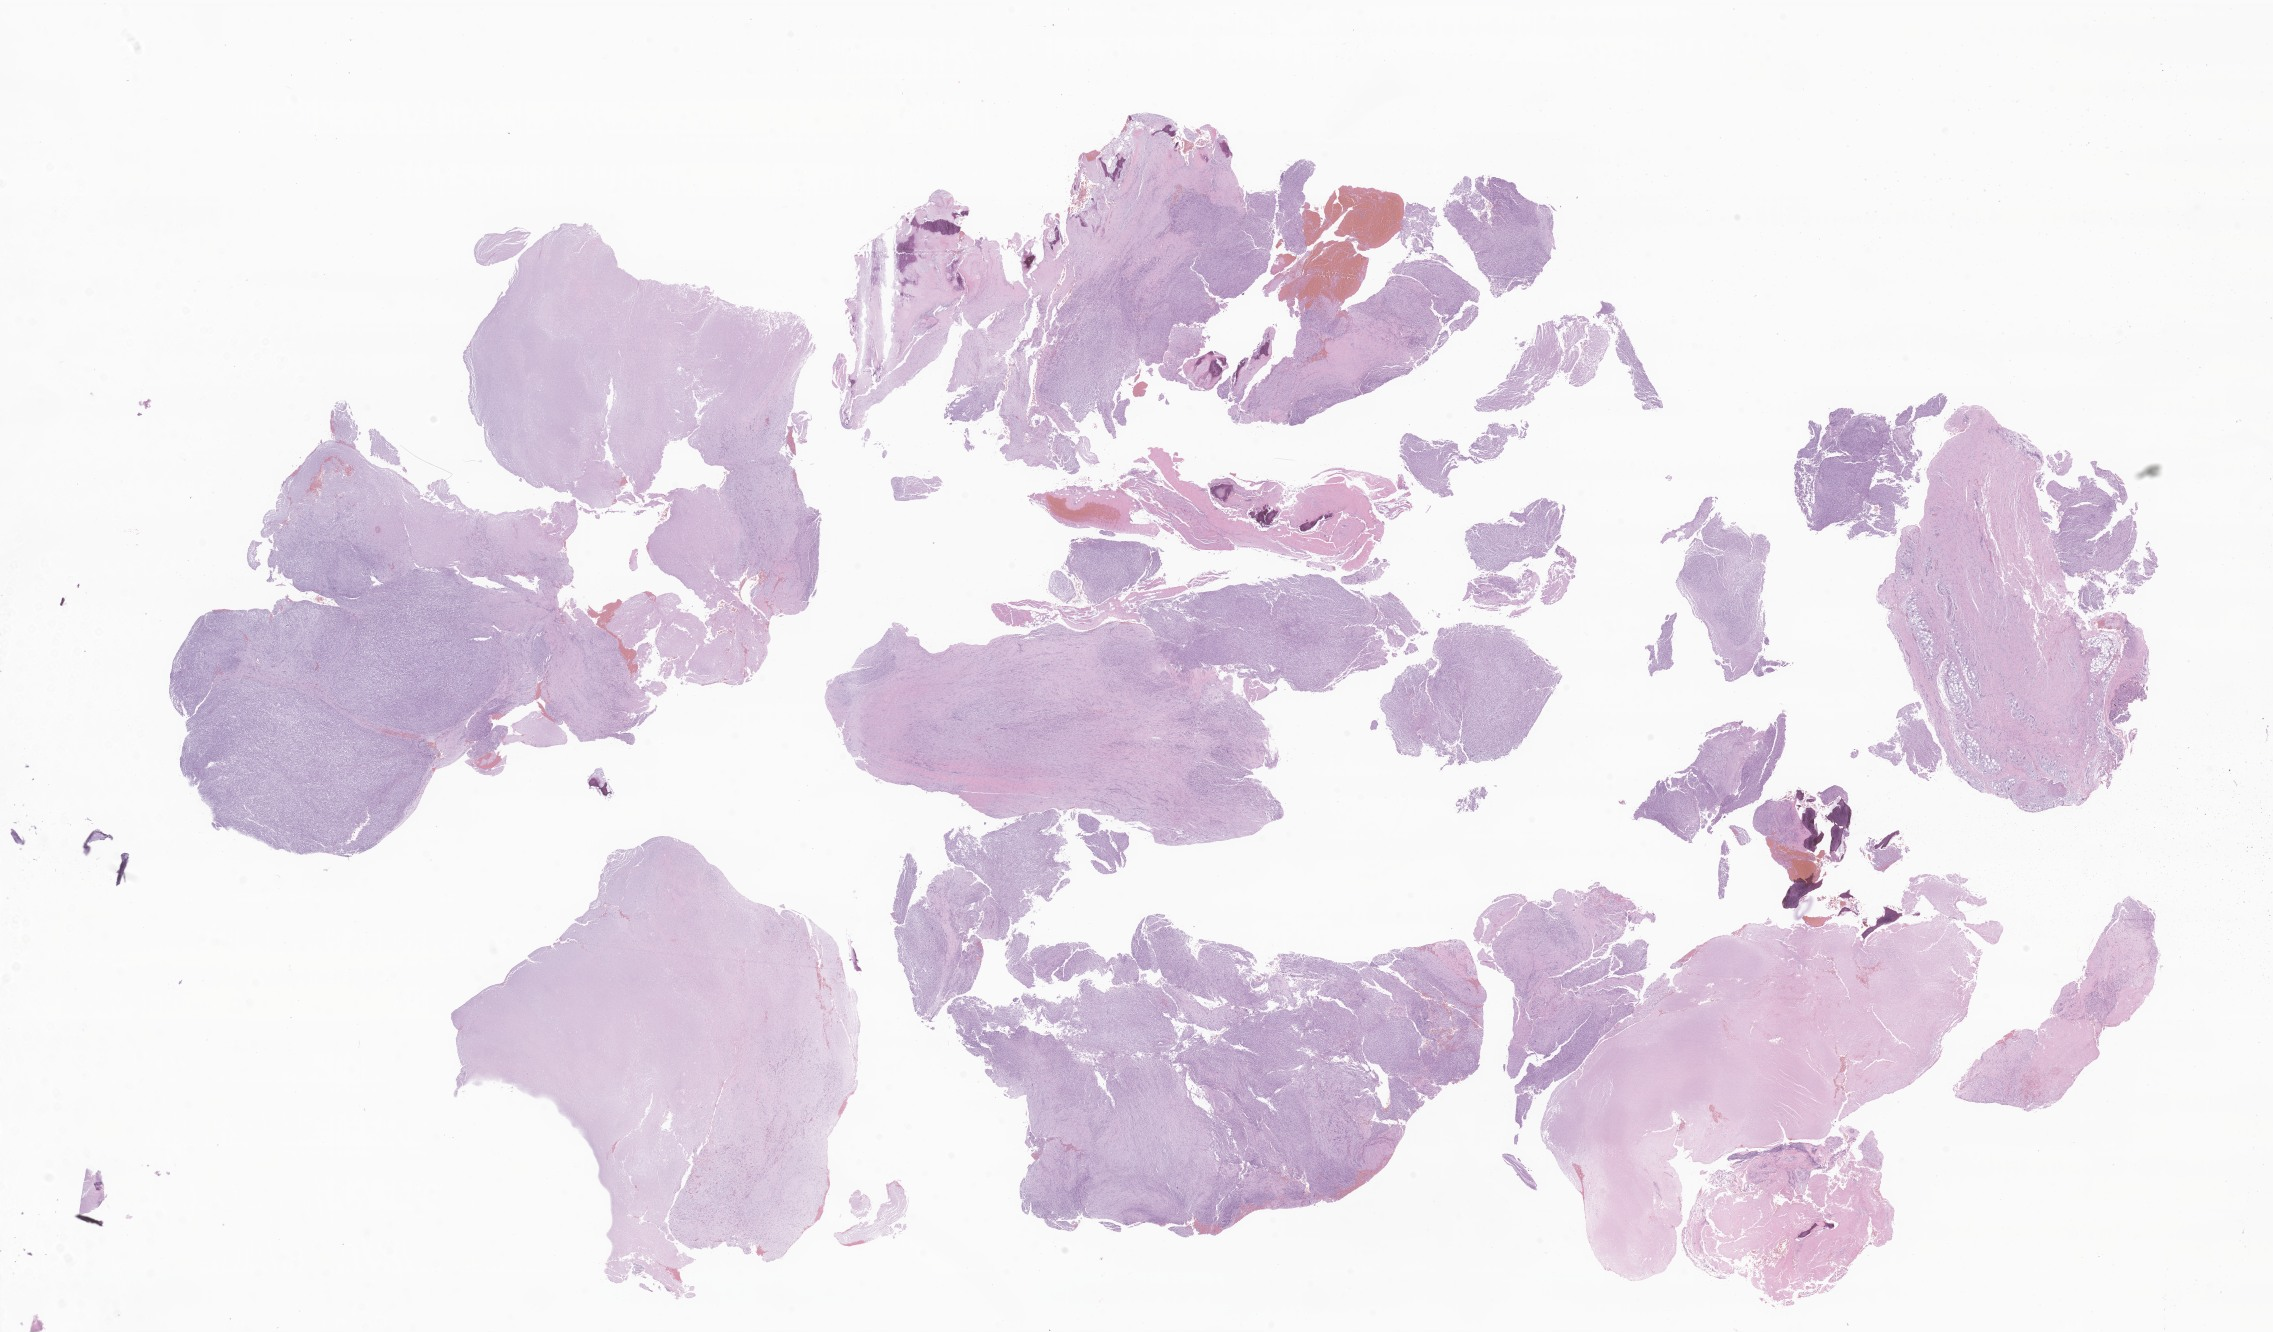
Hematoxylin and eosin (H&E) whole-slide image of tumor tissue from the head and neck, shown as a low-resolution overview of the whole scanned area (about 38.3 x 22.5 mm), FFPE section. Patient: female, age 248 months (20 years 8 months).
Tissue or organ of origin (case record): head, face or neck. Diagnosis: Spindle cell sarcoma.